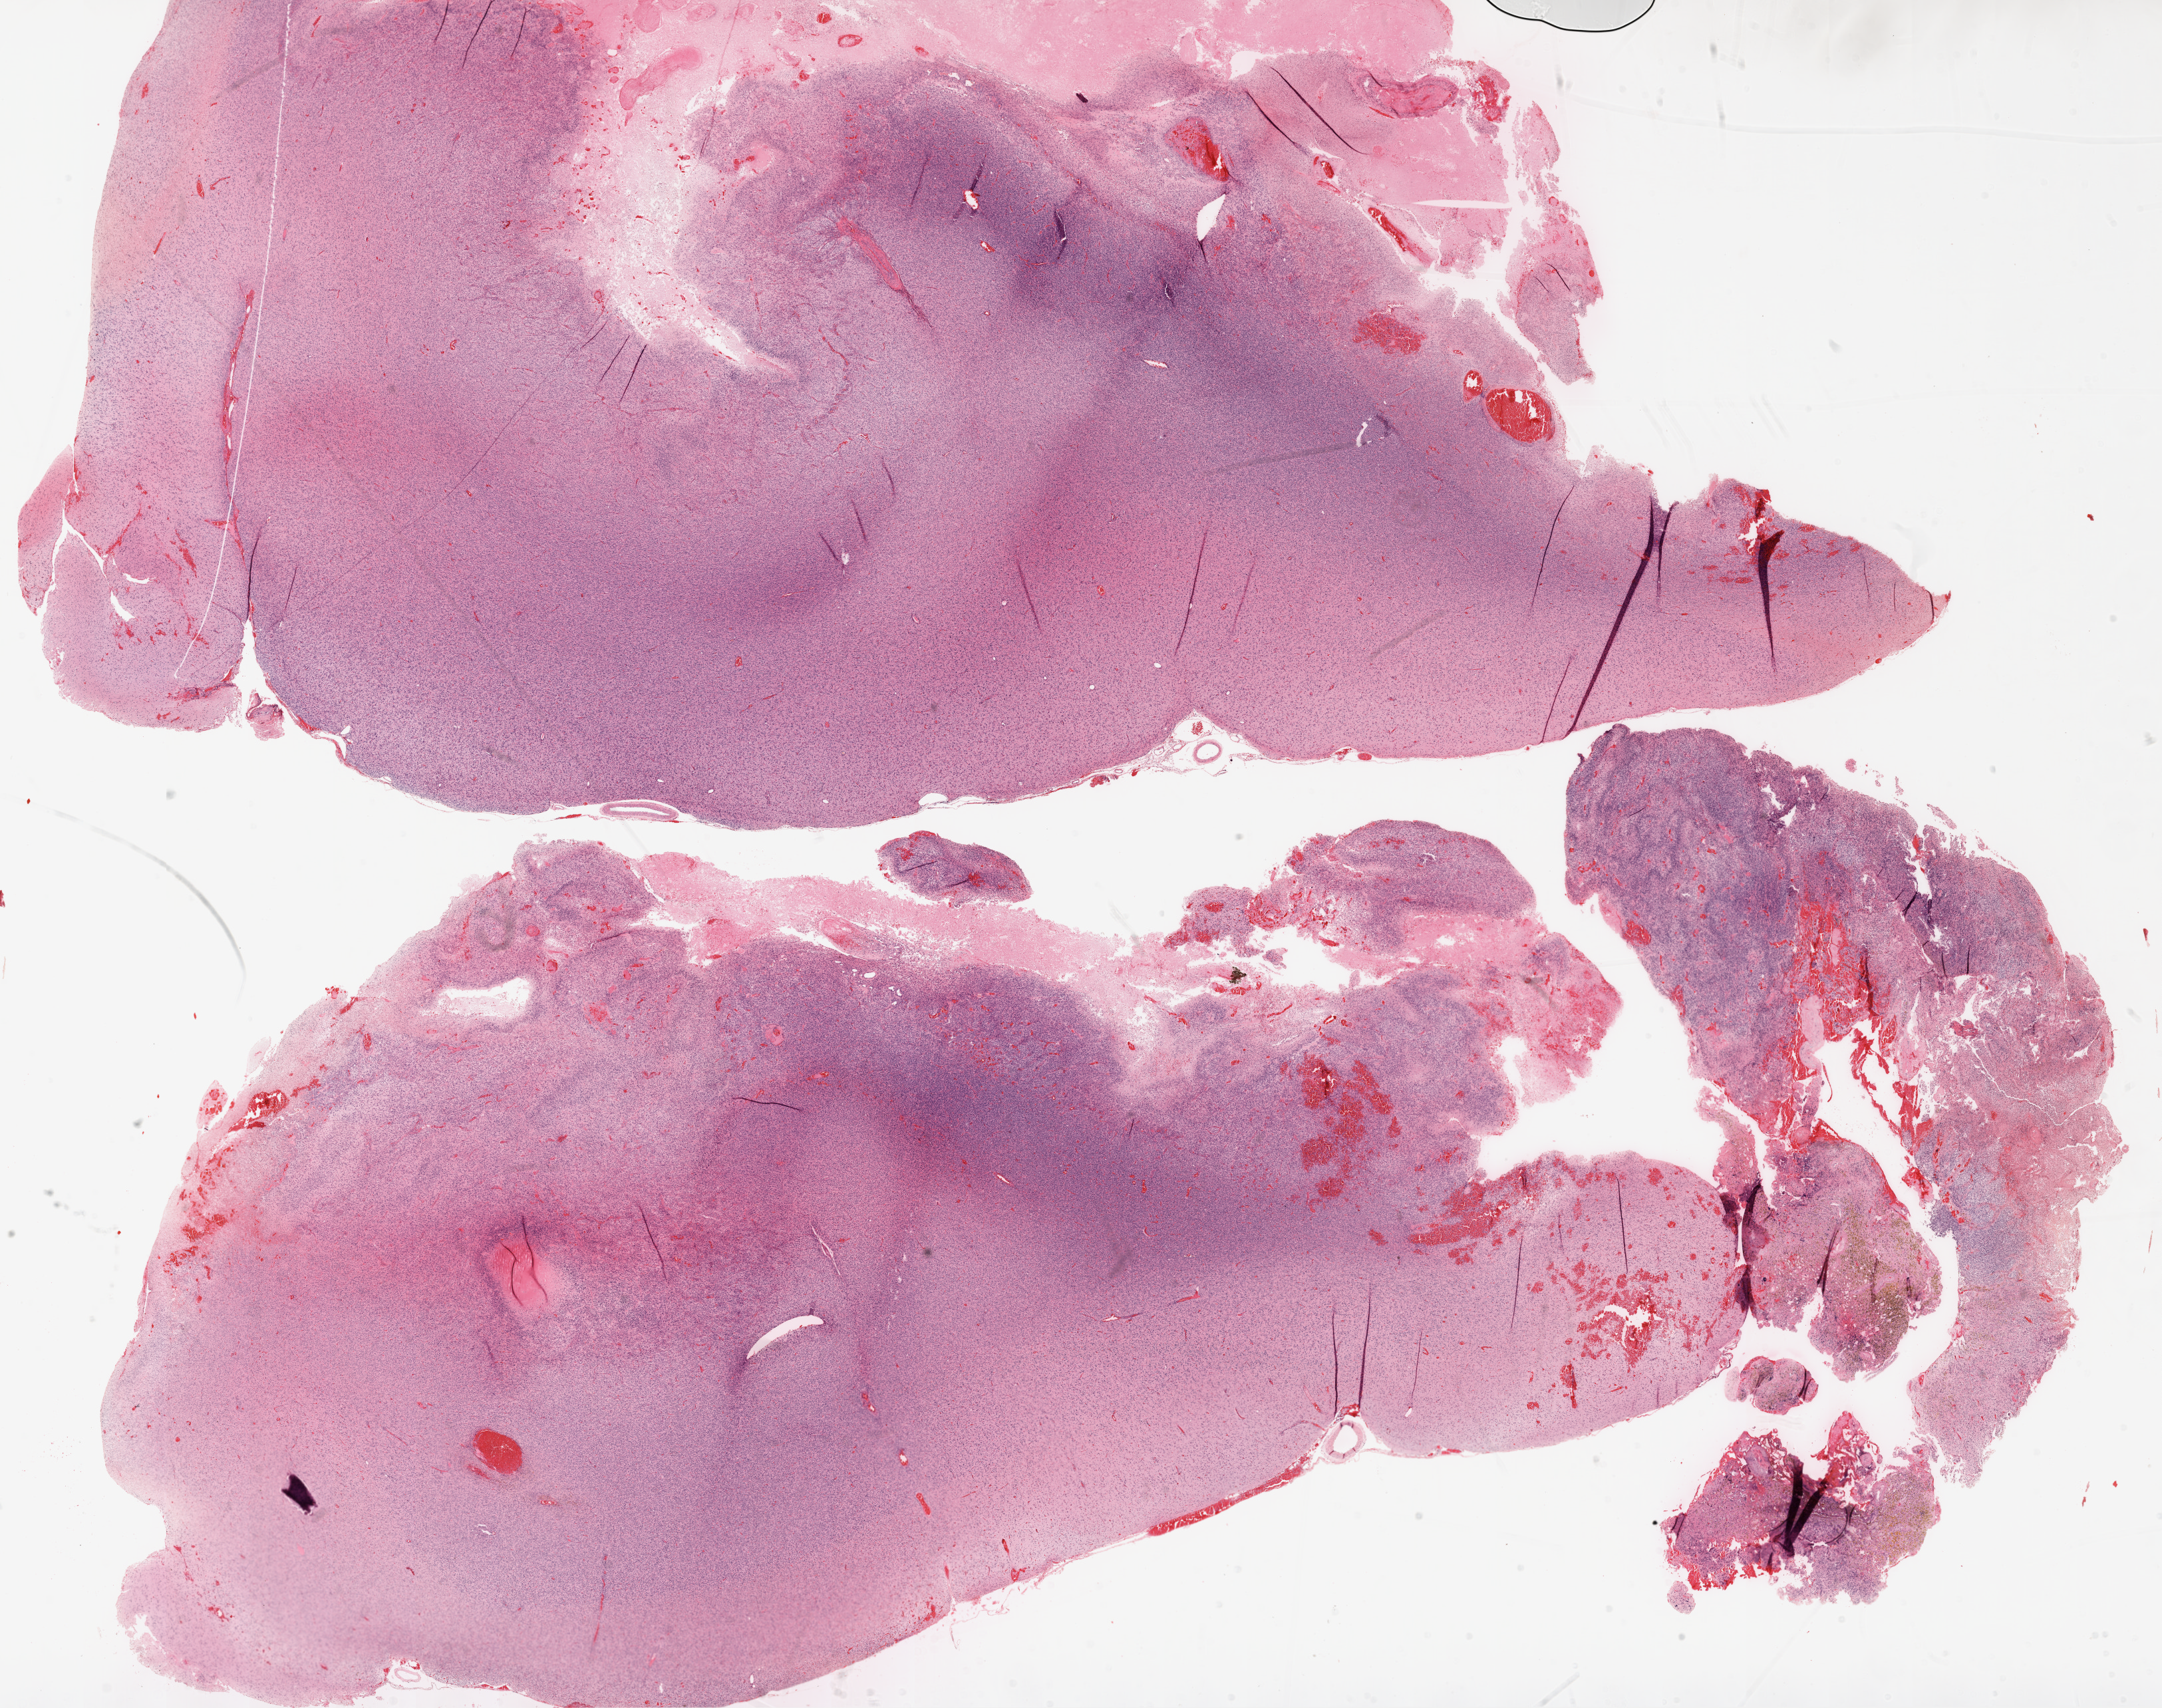
Hematoxylin and eosin (H&E) stained whole-slide image, low-resolution overview of the scanned area, about 26.1 x 20.6 mm; formalin-fixed paraffin-embedded (FFPE) diagnostic section; sample: primary tumour, brain. Female patient; age at initial diagnosis 50 years.
Diagnosis: Glioblastoma.